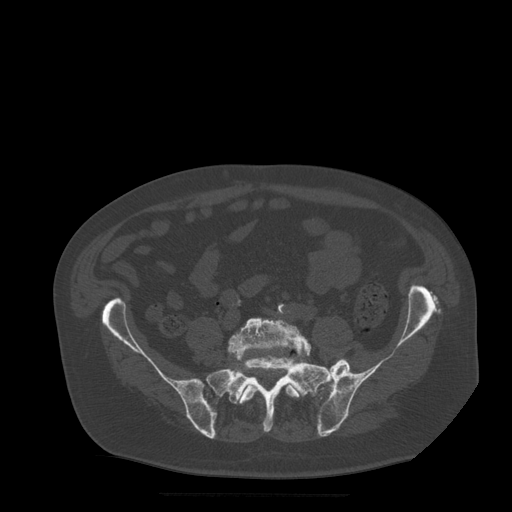
CT including the spine, one axial slice; position 76 of 522 along the scan axis; bone window (W 1800 / L 400 HU); 512 × 512 image matrix. Patient age 72 years. Case-level facts recorded for this patient, not image findings: primary cancer: prostate.
Outlined on this slice (semi-automatically segmented with operator editing):
- L5 vertebra: bounding box [x1, y1, x2, y2] px = [228, 318, 312, 404]